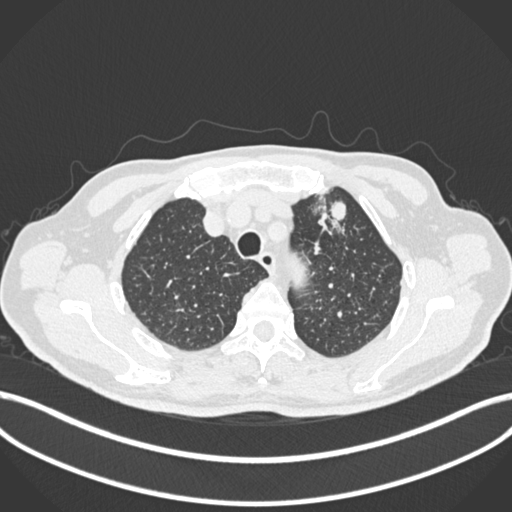
Chest CT, one axial slice. Slice 210 of 261 in the series (ordered by position). Reconstruction kernel B30f. Lung window (W 1500 / L -600 HU). 1 mm slice thickness. 512 × 512 image matrix. Patient: male, 74 years. Case-level facts recorded for this patient, not image findings: clinical TNM (as recorded): T2b N0 M1c.
Structures marked on this image (bounding box drawn by a radiologist):
- lung tumour (recorded histology: adenocarcinoma): bounding box <311,189,355,237> (left, top, right, bottom; pixels)